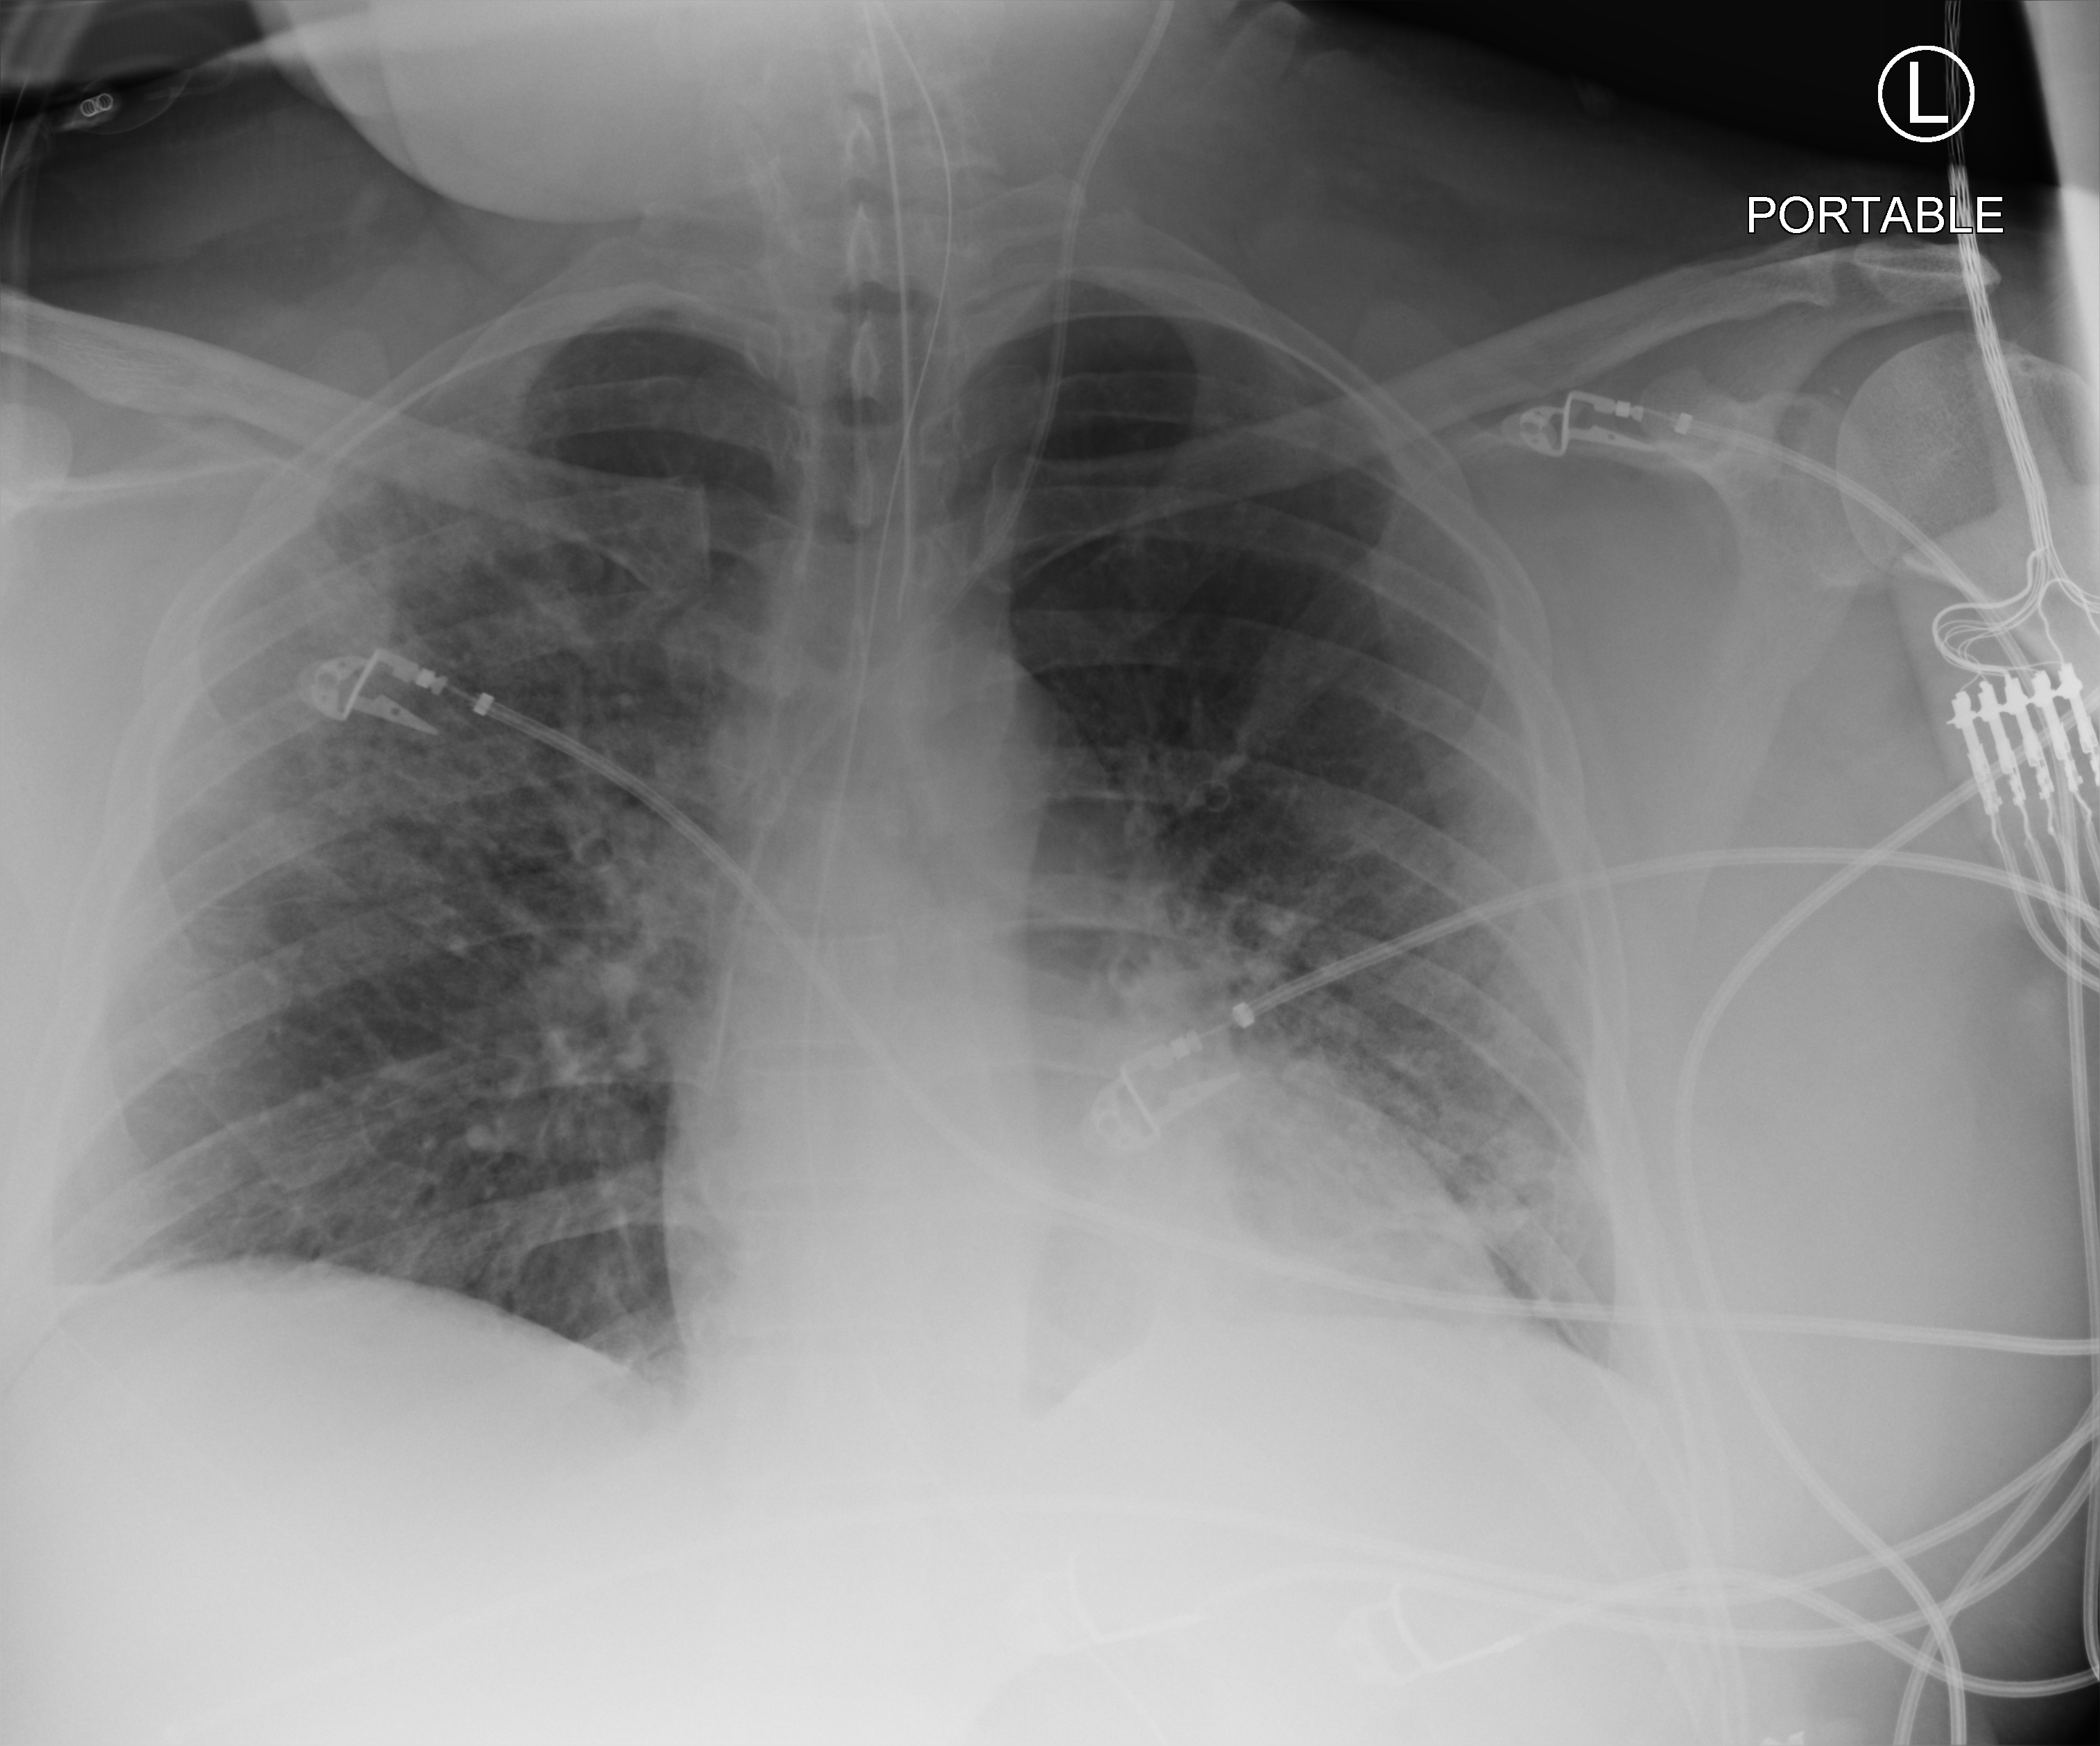
Bedside chest radiograph (computed radiography). Adult patient hospitalised with COVID-19, age 18–59 years.
From the hospital-stay record, not from the radiograph (when in the stay this image was taken is not recorded): chronic kidney disease (admission record): no; admitted to intensive care during this hospital stay: yes; other chronic lung disease (admission record): yes.